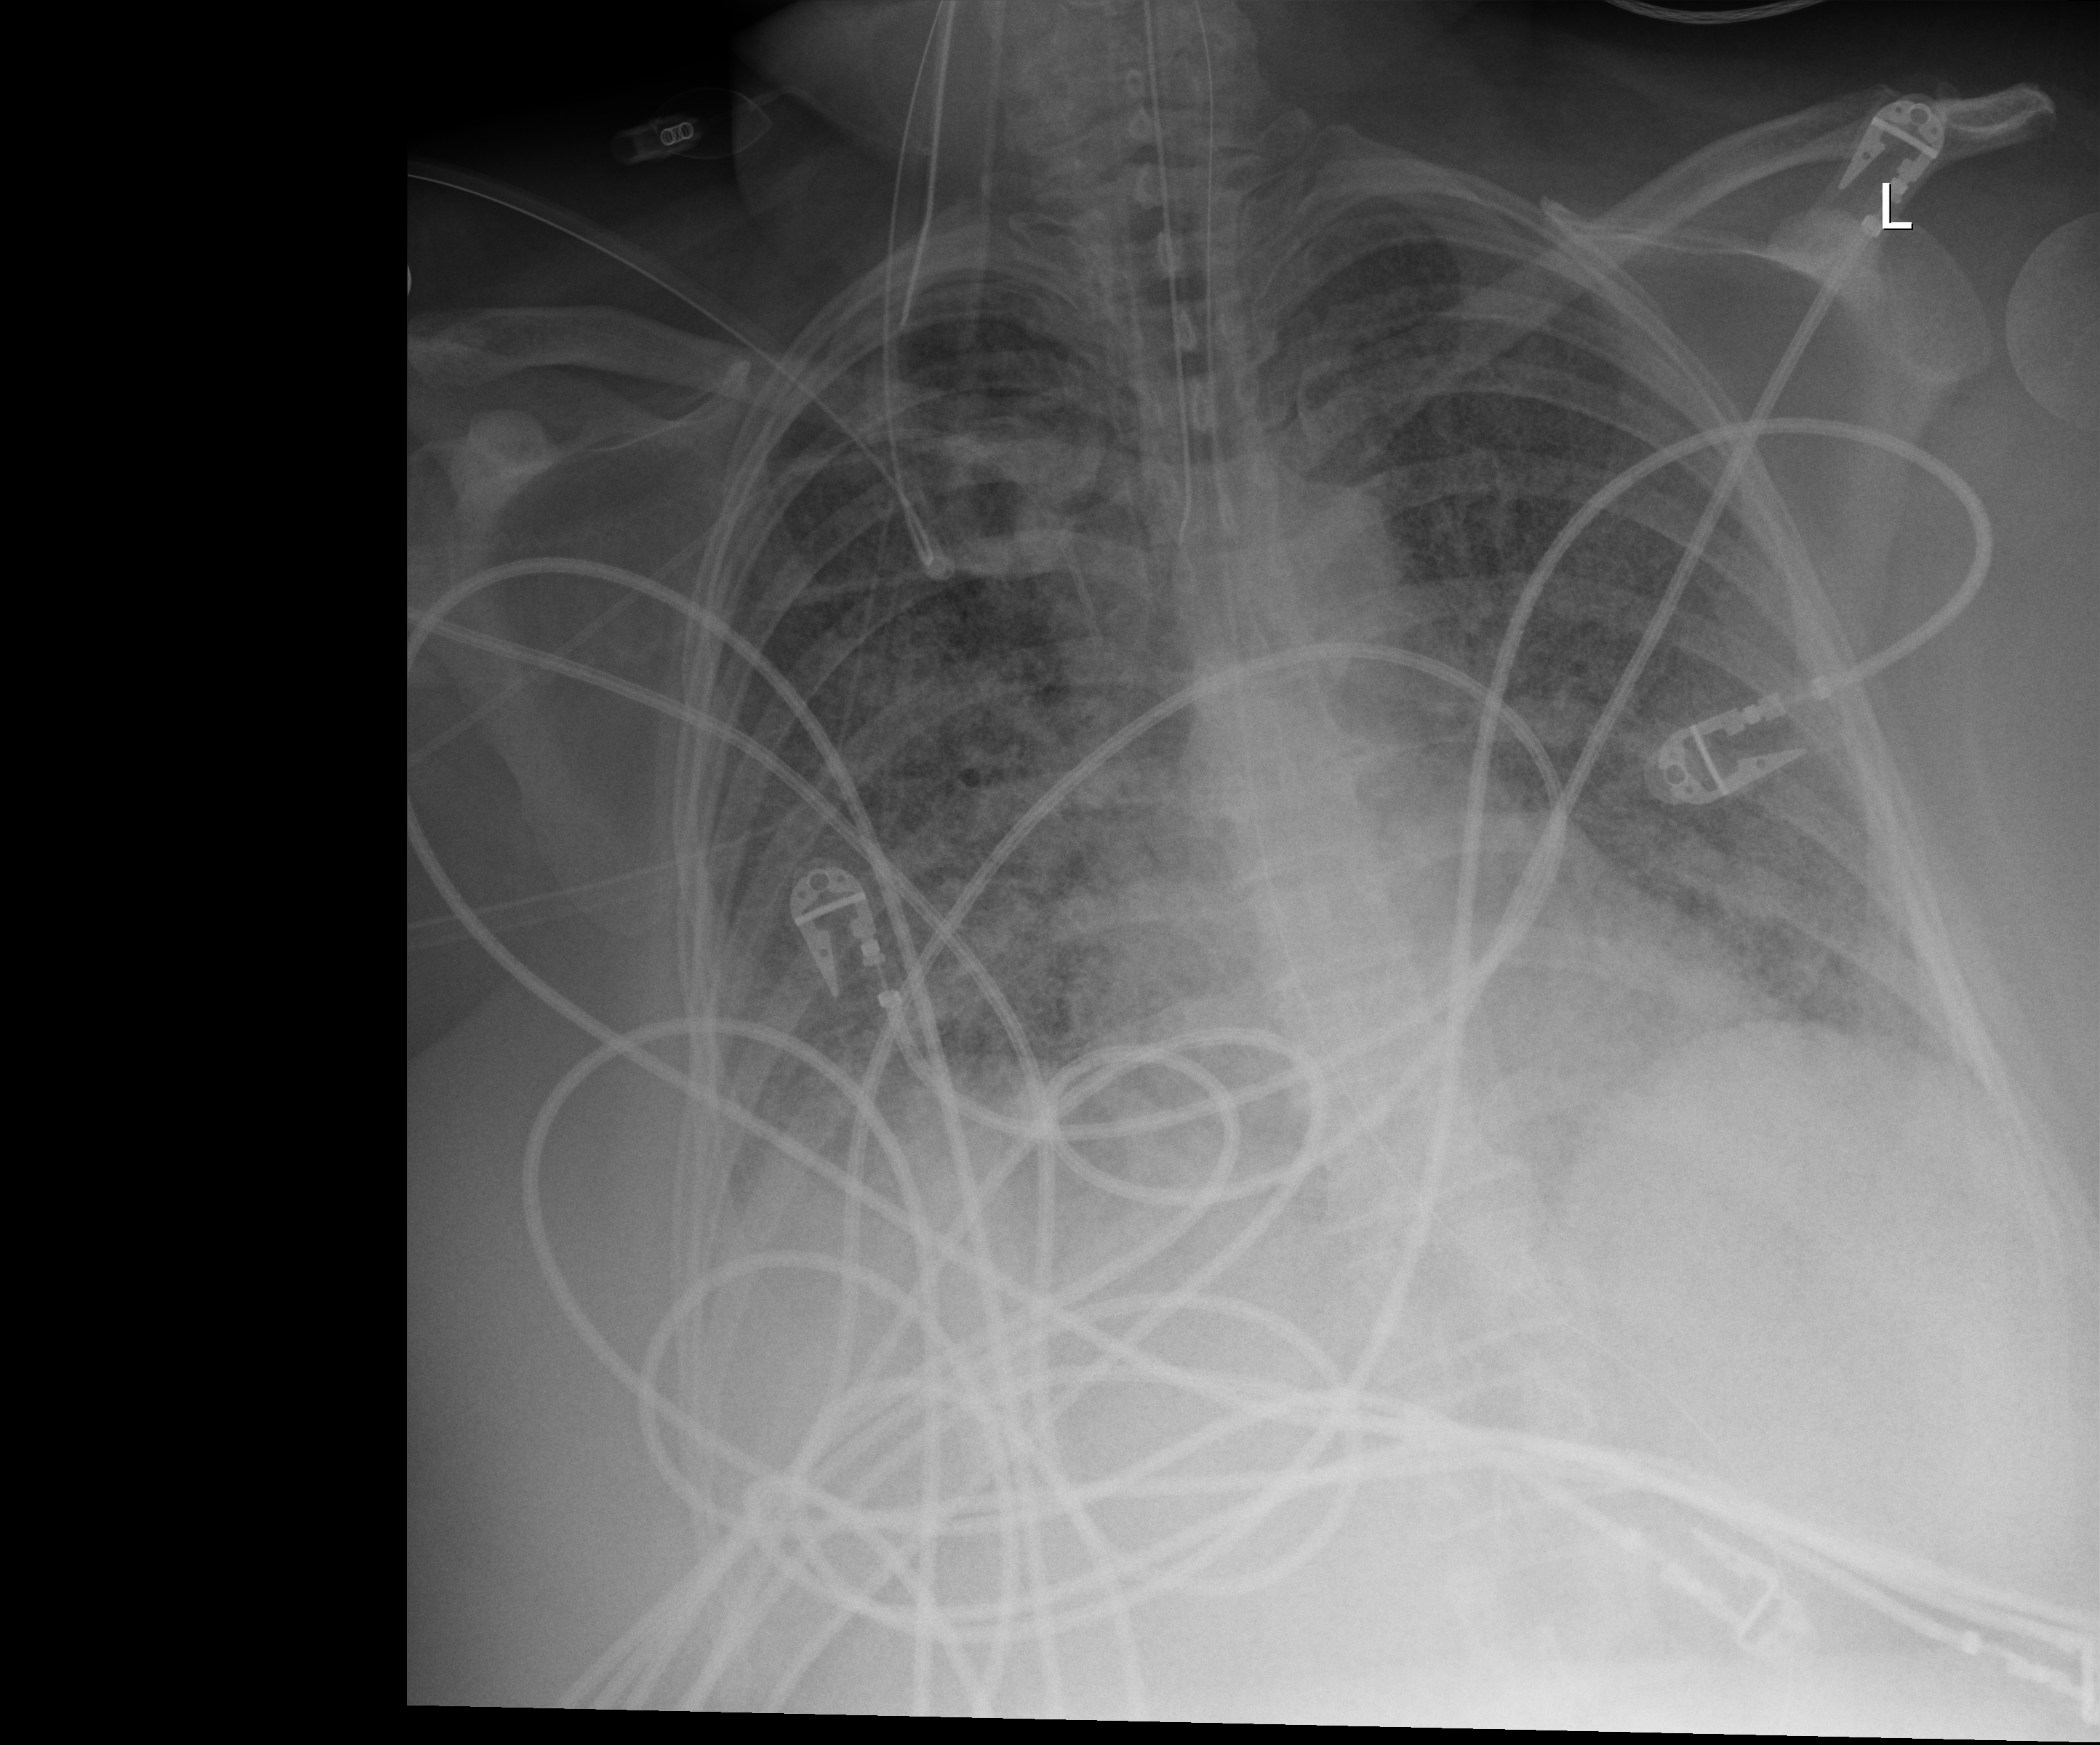
Chest X-ray (portable); anteroposterior (AP) projection. Female patient hospitalised with COVID-19, age 18–59 years.
From the hospital-stay record, not from the radiograph (when in the stay this image was taken is not recorded):
- admitted to intensive care during this hospital stay: yes
- mechanically ventilated during this hospital stay: yes